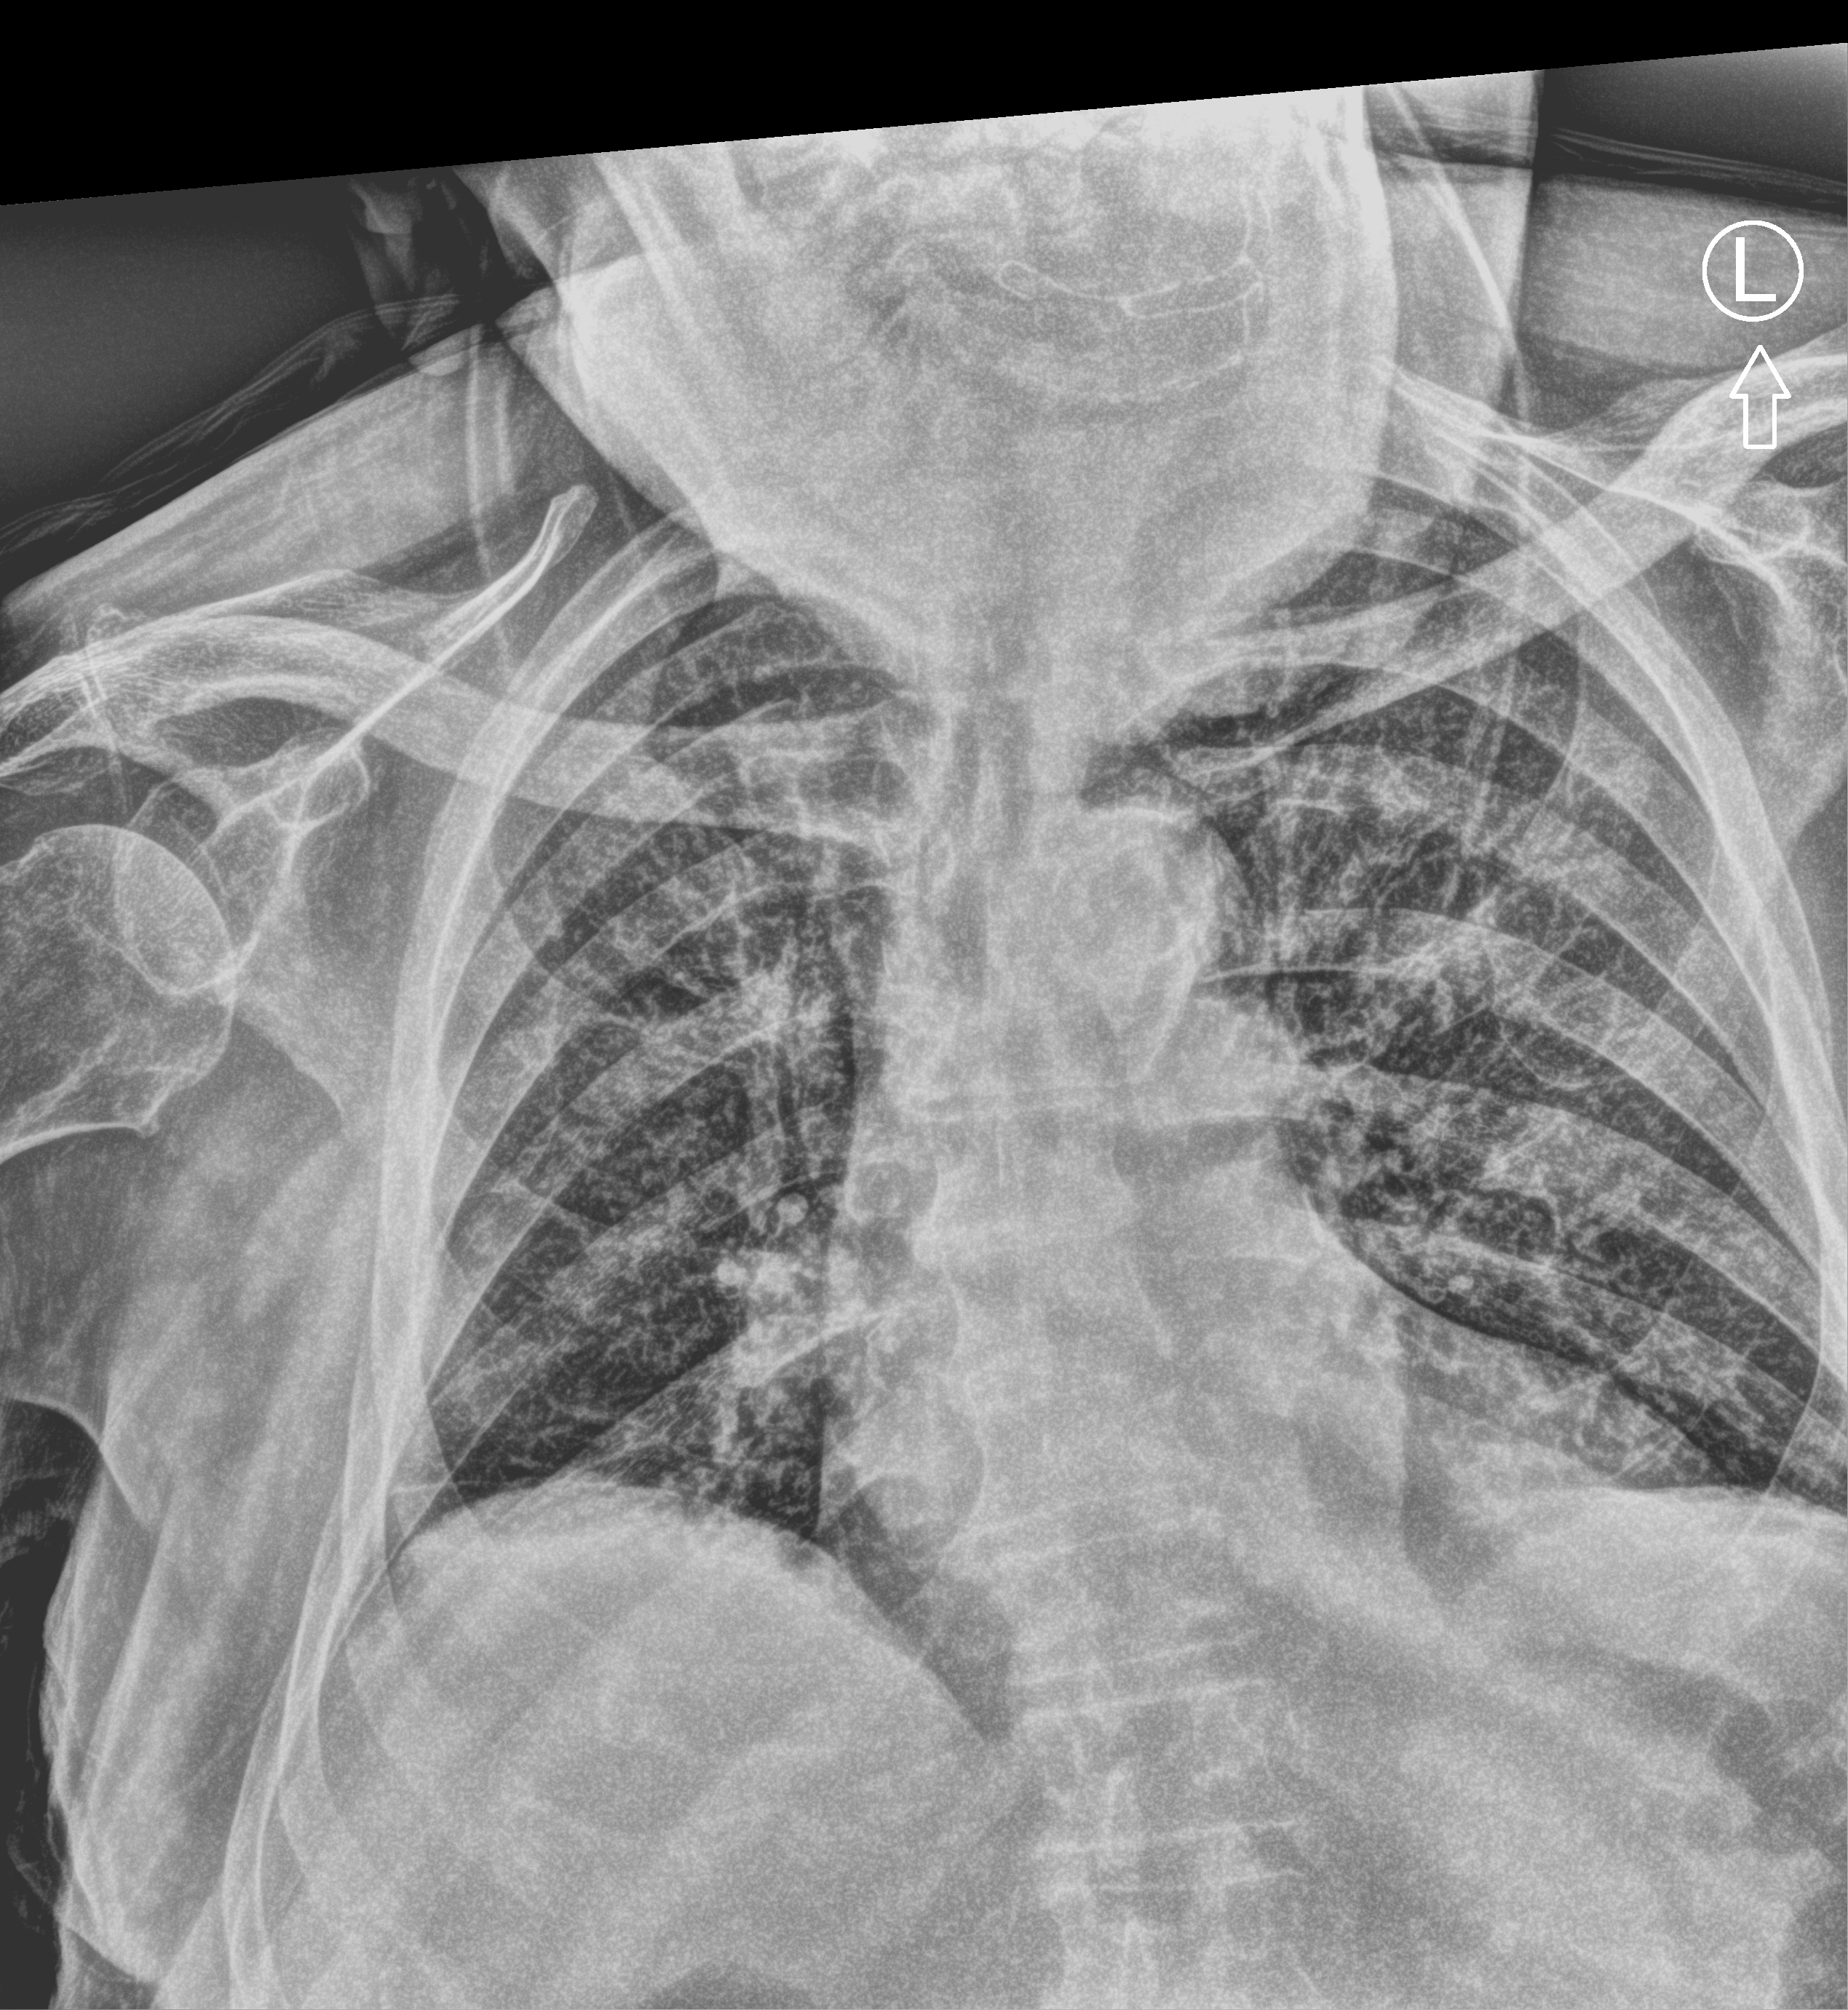
Portable chest radiograph; anteroposterior (AP) projection. Male patient hospitalised with COVID-19, age 75–90 years.
Admission-level facts for this patient (not findings on this image; timing relative to this image not recorded): mechanically ventilated during this hospital stay: yes.